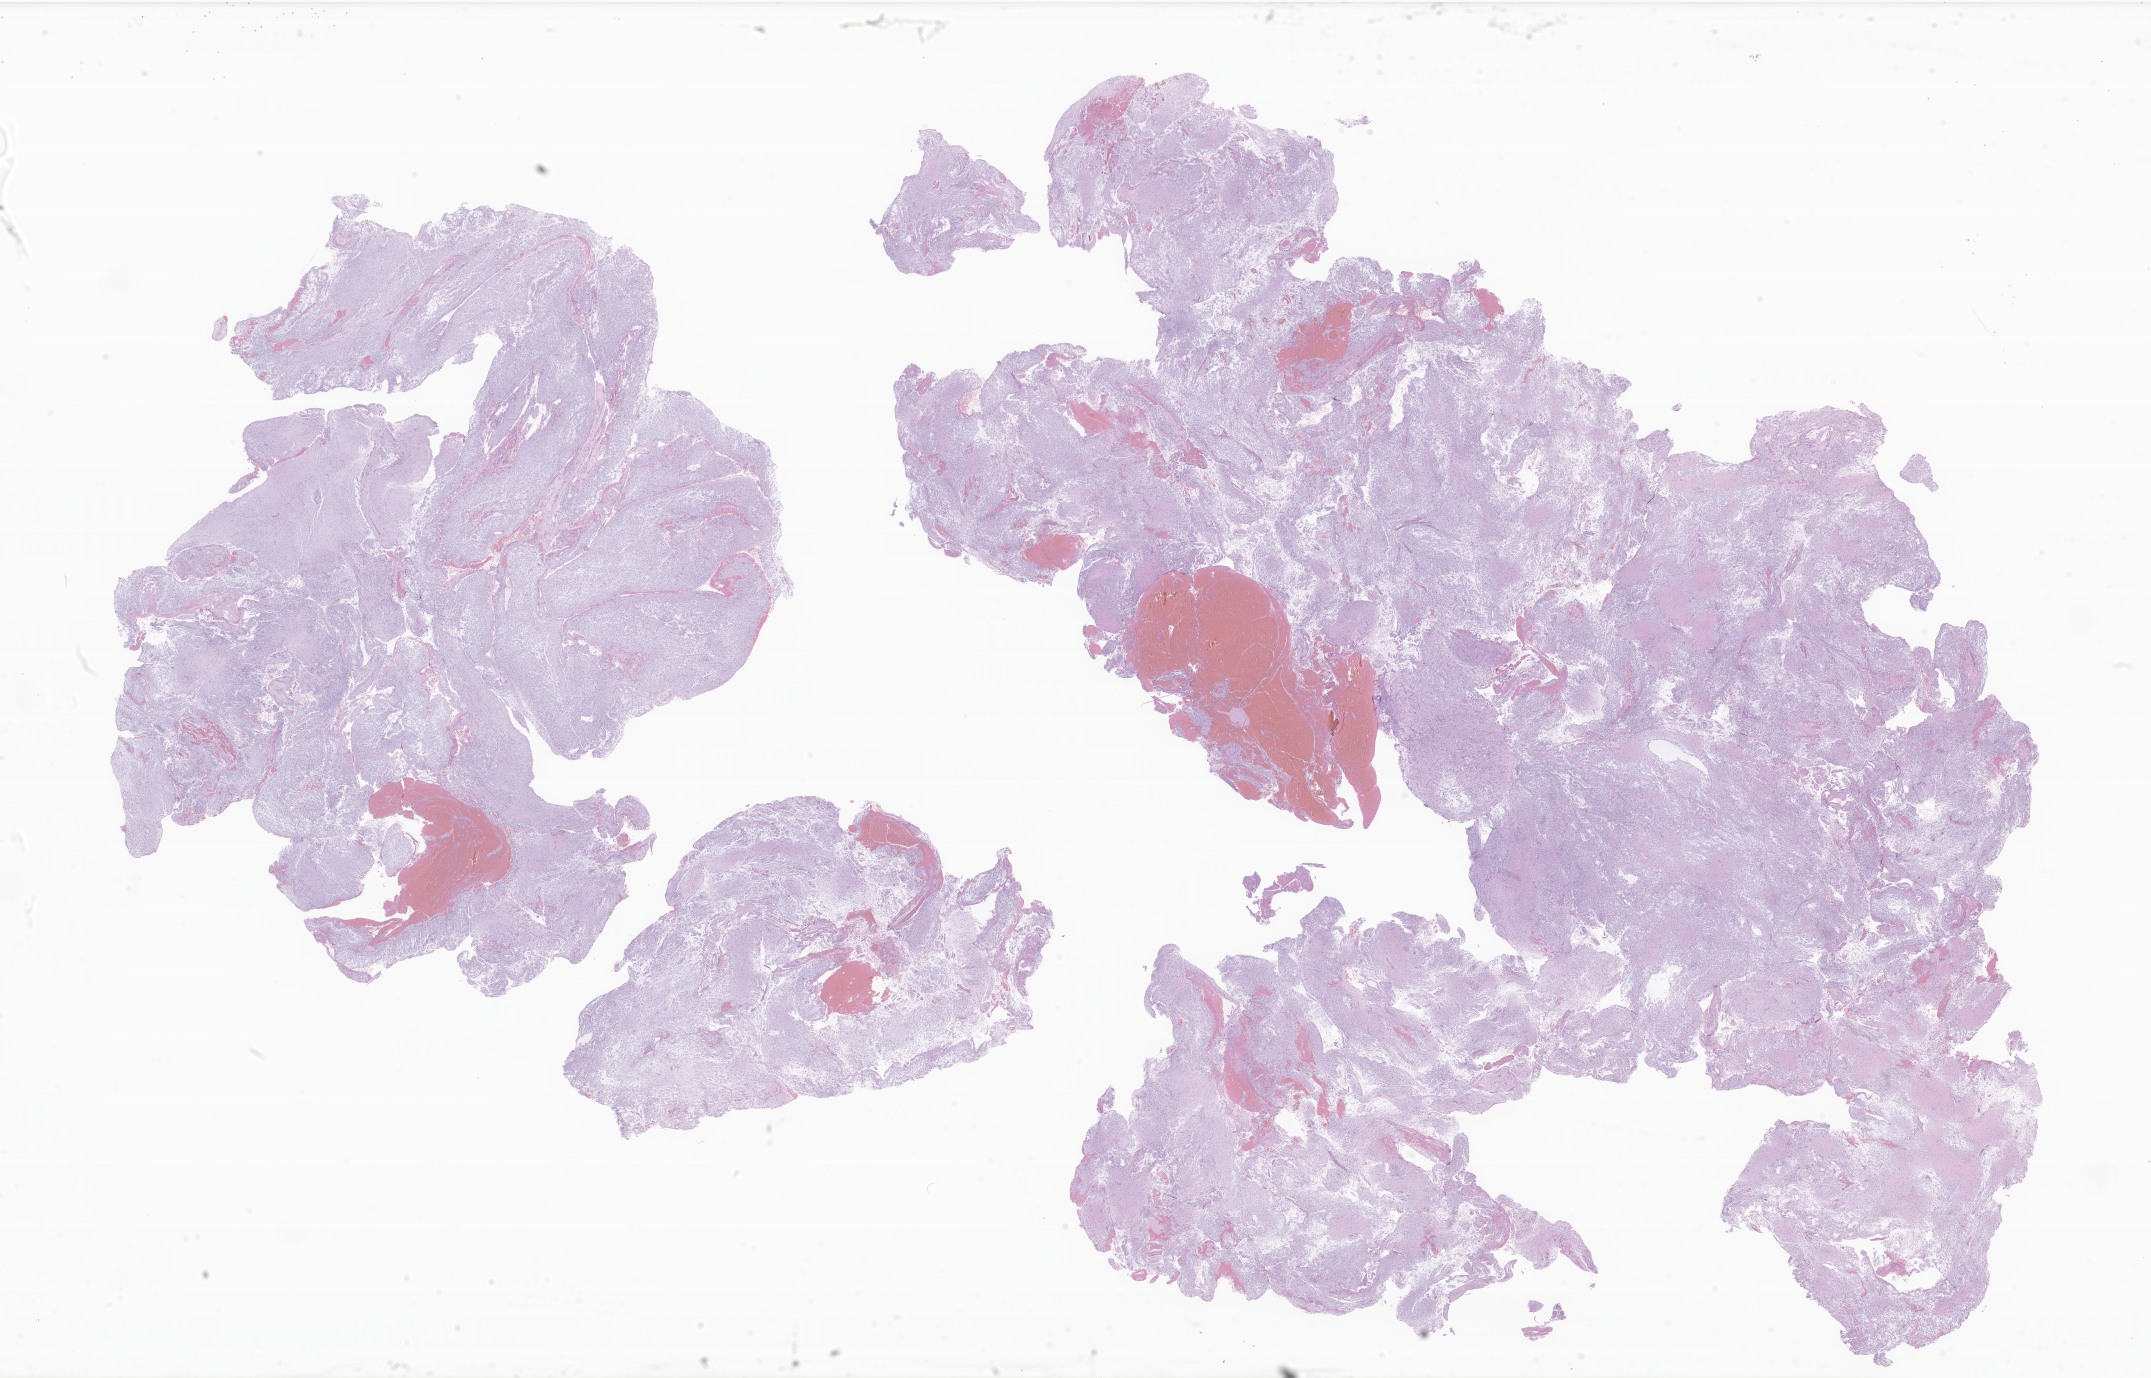
Digitized hematoxylin and eosin (H&E)-stained section of tumor tissue from the brain, shown as a low-resolution overview of the whole scanned area (about 36.3 x 23.2 mm), formalin-fixed, paraffin-embedded (FFPE) tissue. Female patient, age 90 months.
Diagnosis (ICD-O-3 morphology term): Pilocytic astrocytoma.